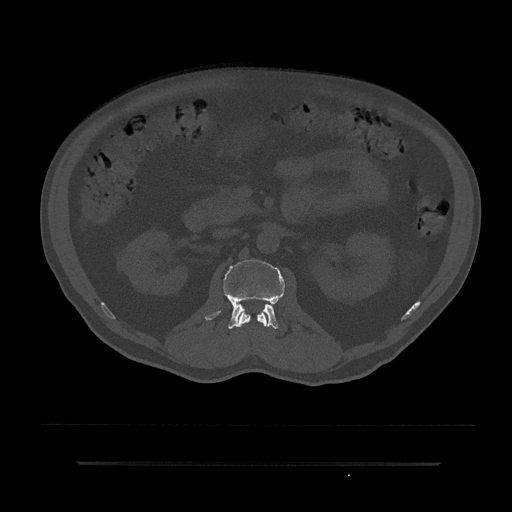
CT including the spine, one axial slice; position 100 of 797 along the scan axis; bone window (W 1800 / L 400 HU); 0.5 mm slice thickness; 512 × 512 image matrix. Male patient, age 59 years. Case-level facts recorded for this patient, not image findings: primary cancer: bile ducts.
Annotated regions visible in this slice (semi-automatic segmentation, software-assisted and operator-edited):
- L1 vertebra: bounding box [x1, y1, x2, y2] px = [237, 311, 268, 327]
- L2 vertebra: [205, 259, 285, 329]